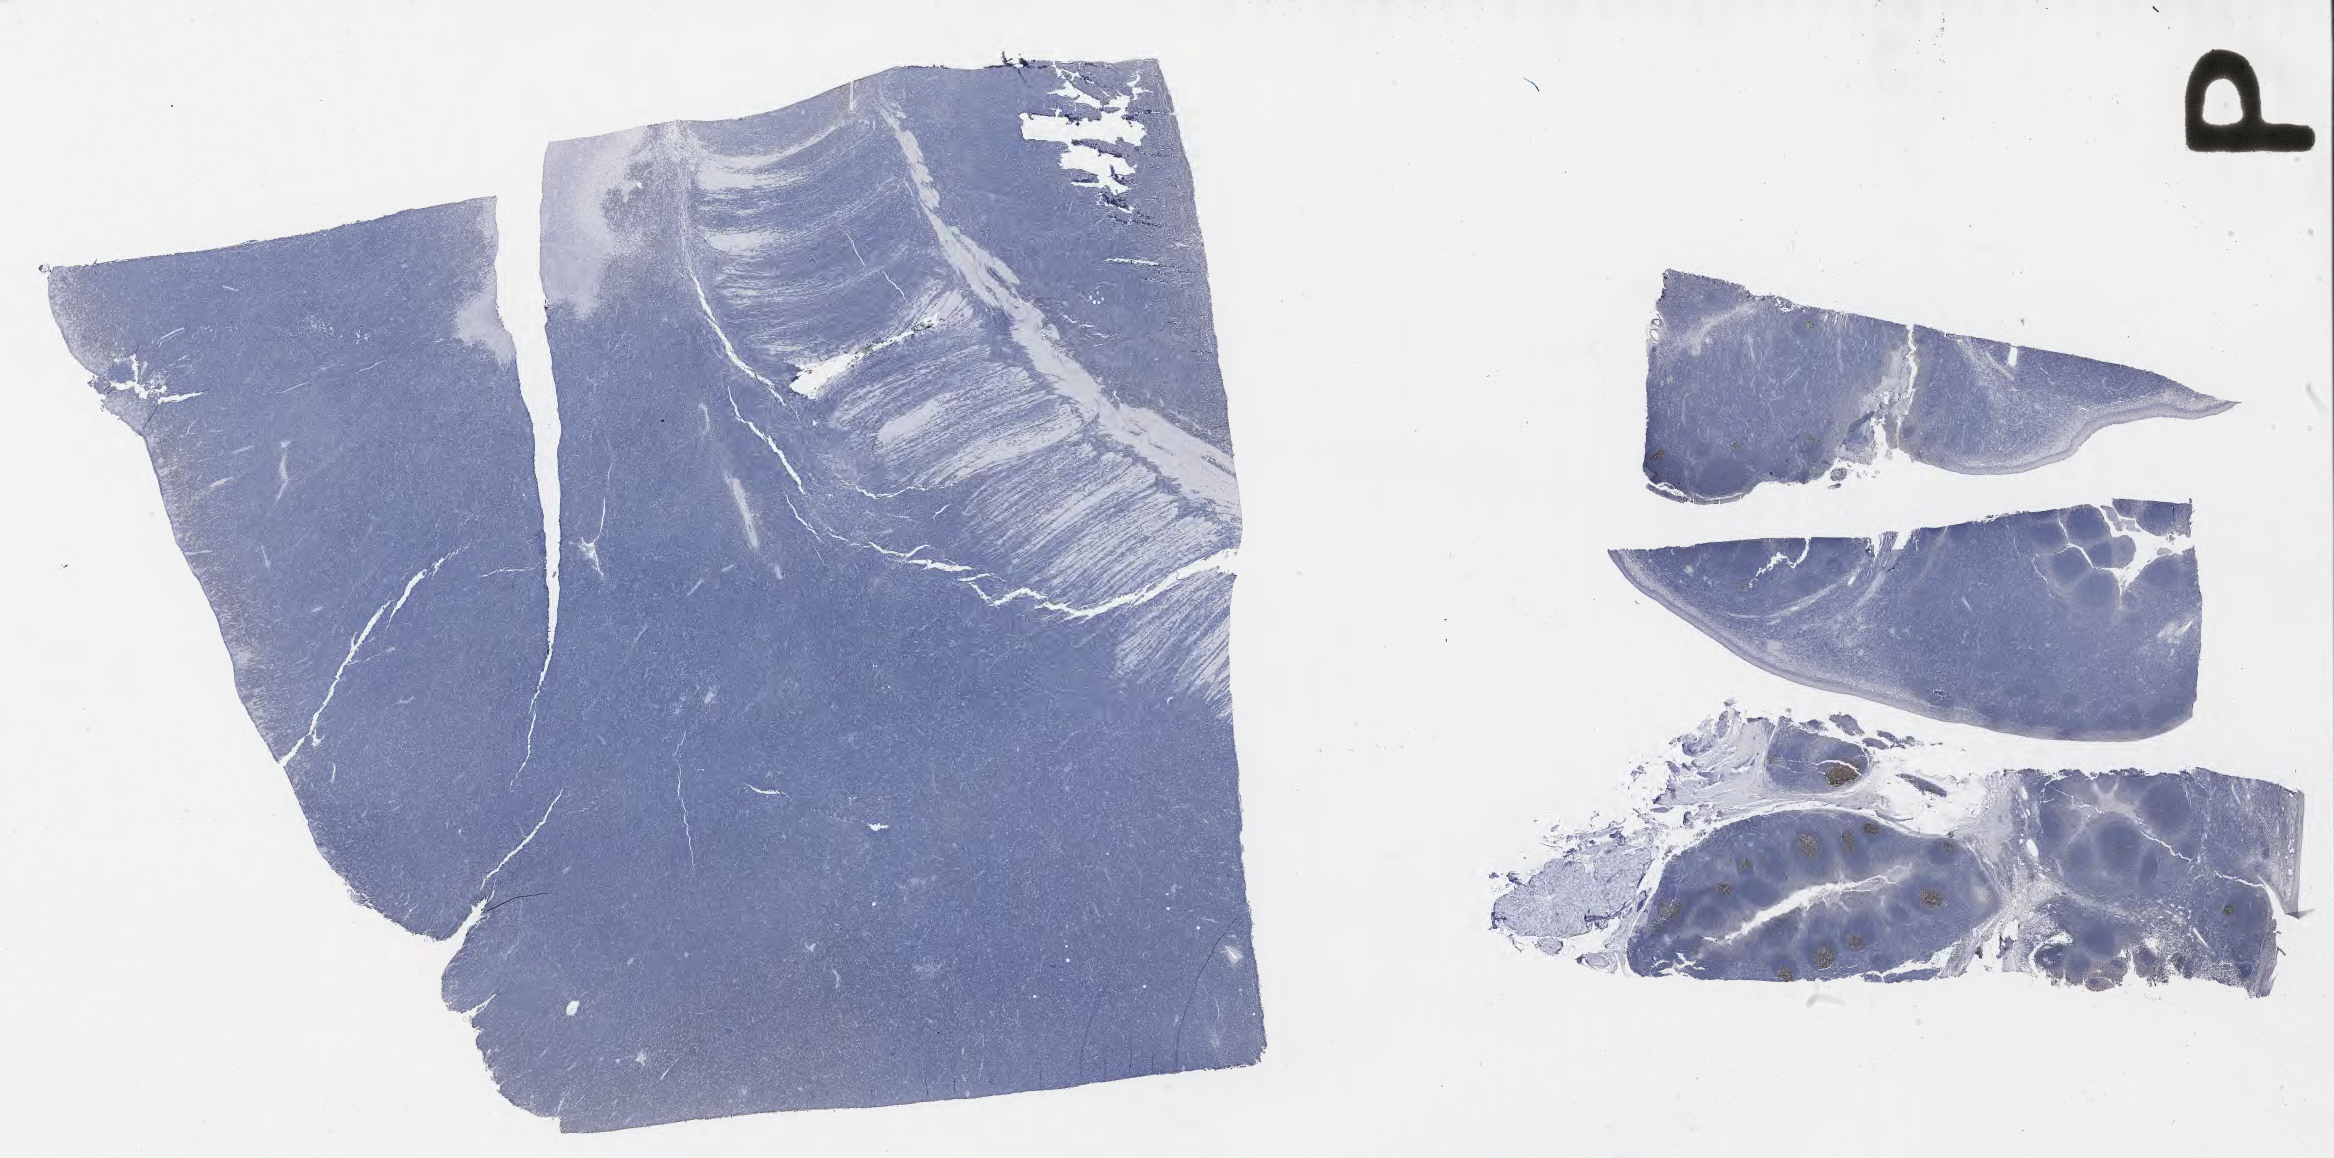
Immunohistochemistry (IHC) whole-slide image stained for BCL6 — shown as a low-resolution overview of the whole scanned area (about 37.7 x 18.7 mm). Tumor tissue. Site: colon. Patient: male, 14 years old.
Histologic diagnosis: Burkitt lymphoma, NOS.